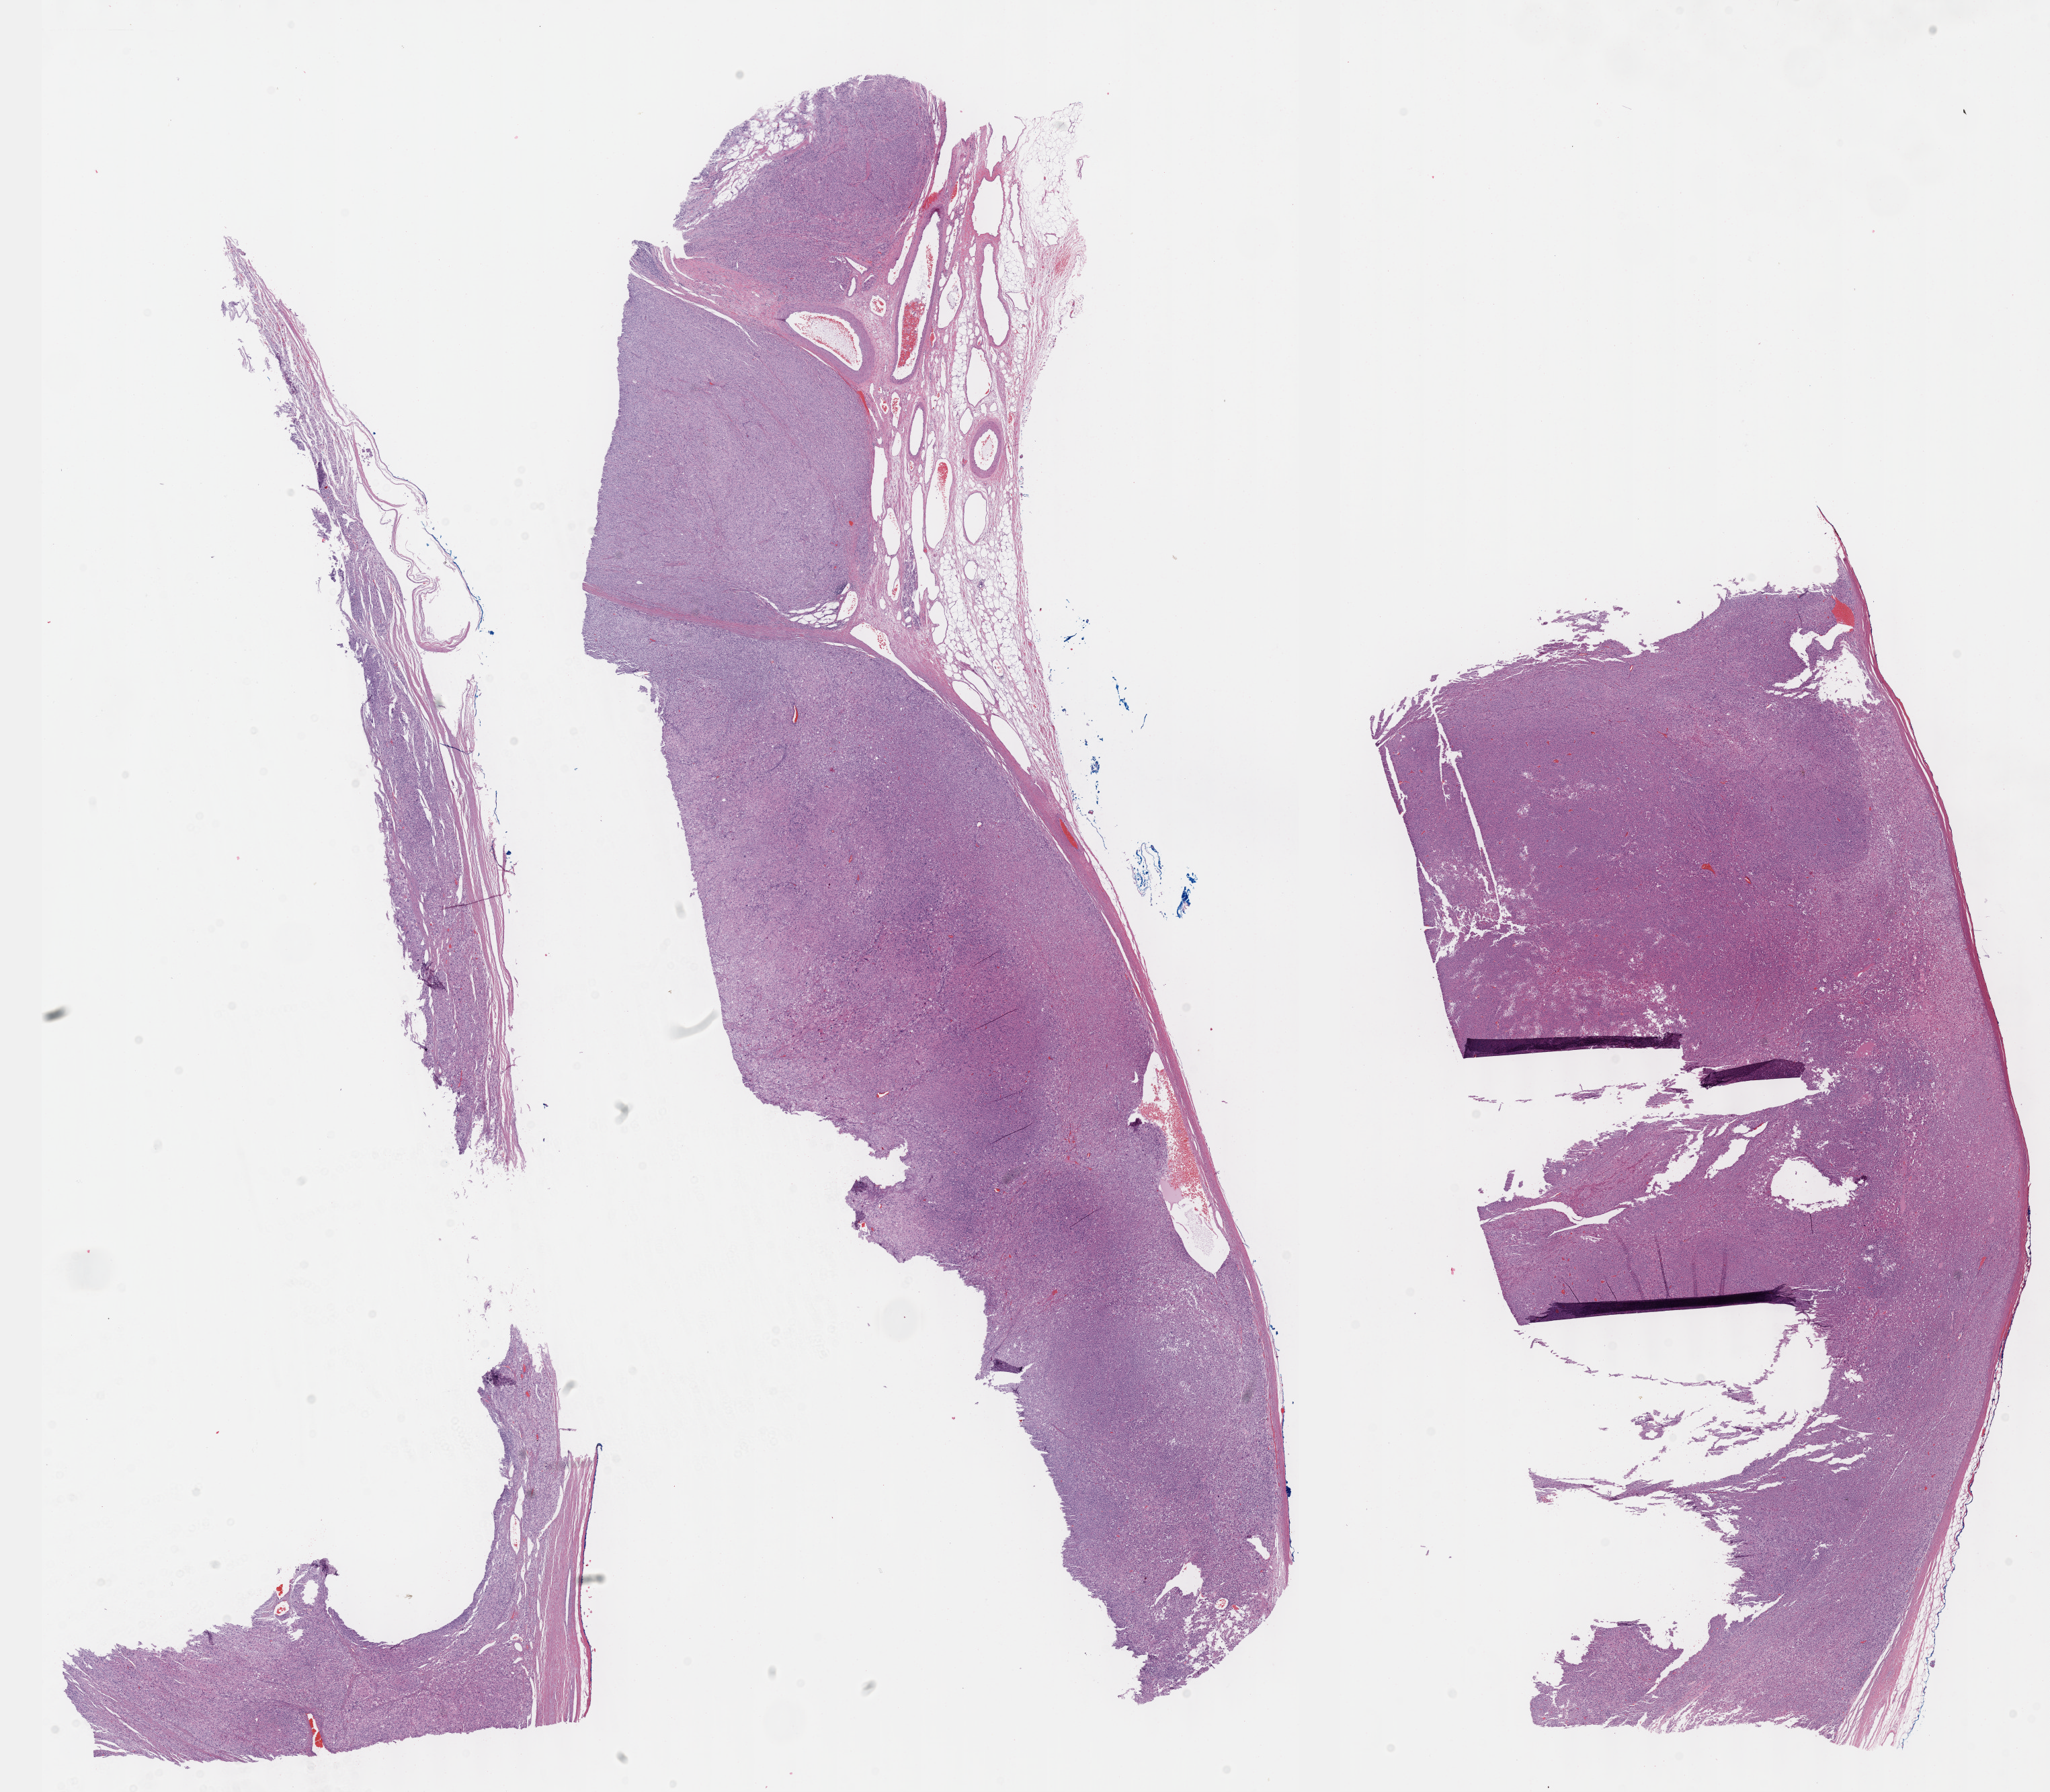
Digitized H&E-stained tissue section (whole slide) — a low-resolution overview of the entire scanned area, about 24.6 x 21.5 mm (acquisition: 40x scan). Formalin-fixed paraffin-embedded (FFPE) diagnostic section. Primary tumour sample from the adrenal cortex. Patient: female, age at initial diagnosis 53 years.
Lymph nodes positive (case pathology): 3 of 3 examined. Diagnosis: Adrenal cortical carcinoma (cortex of adrenal gland).